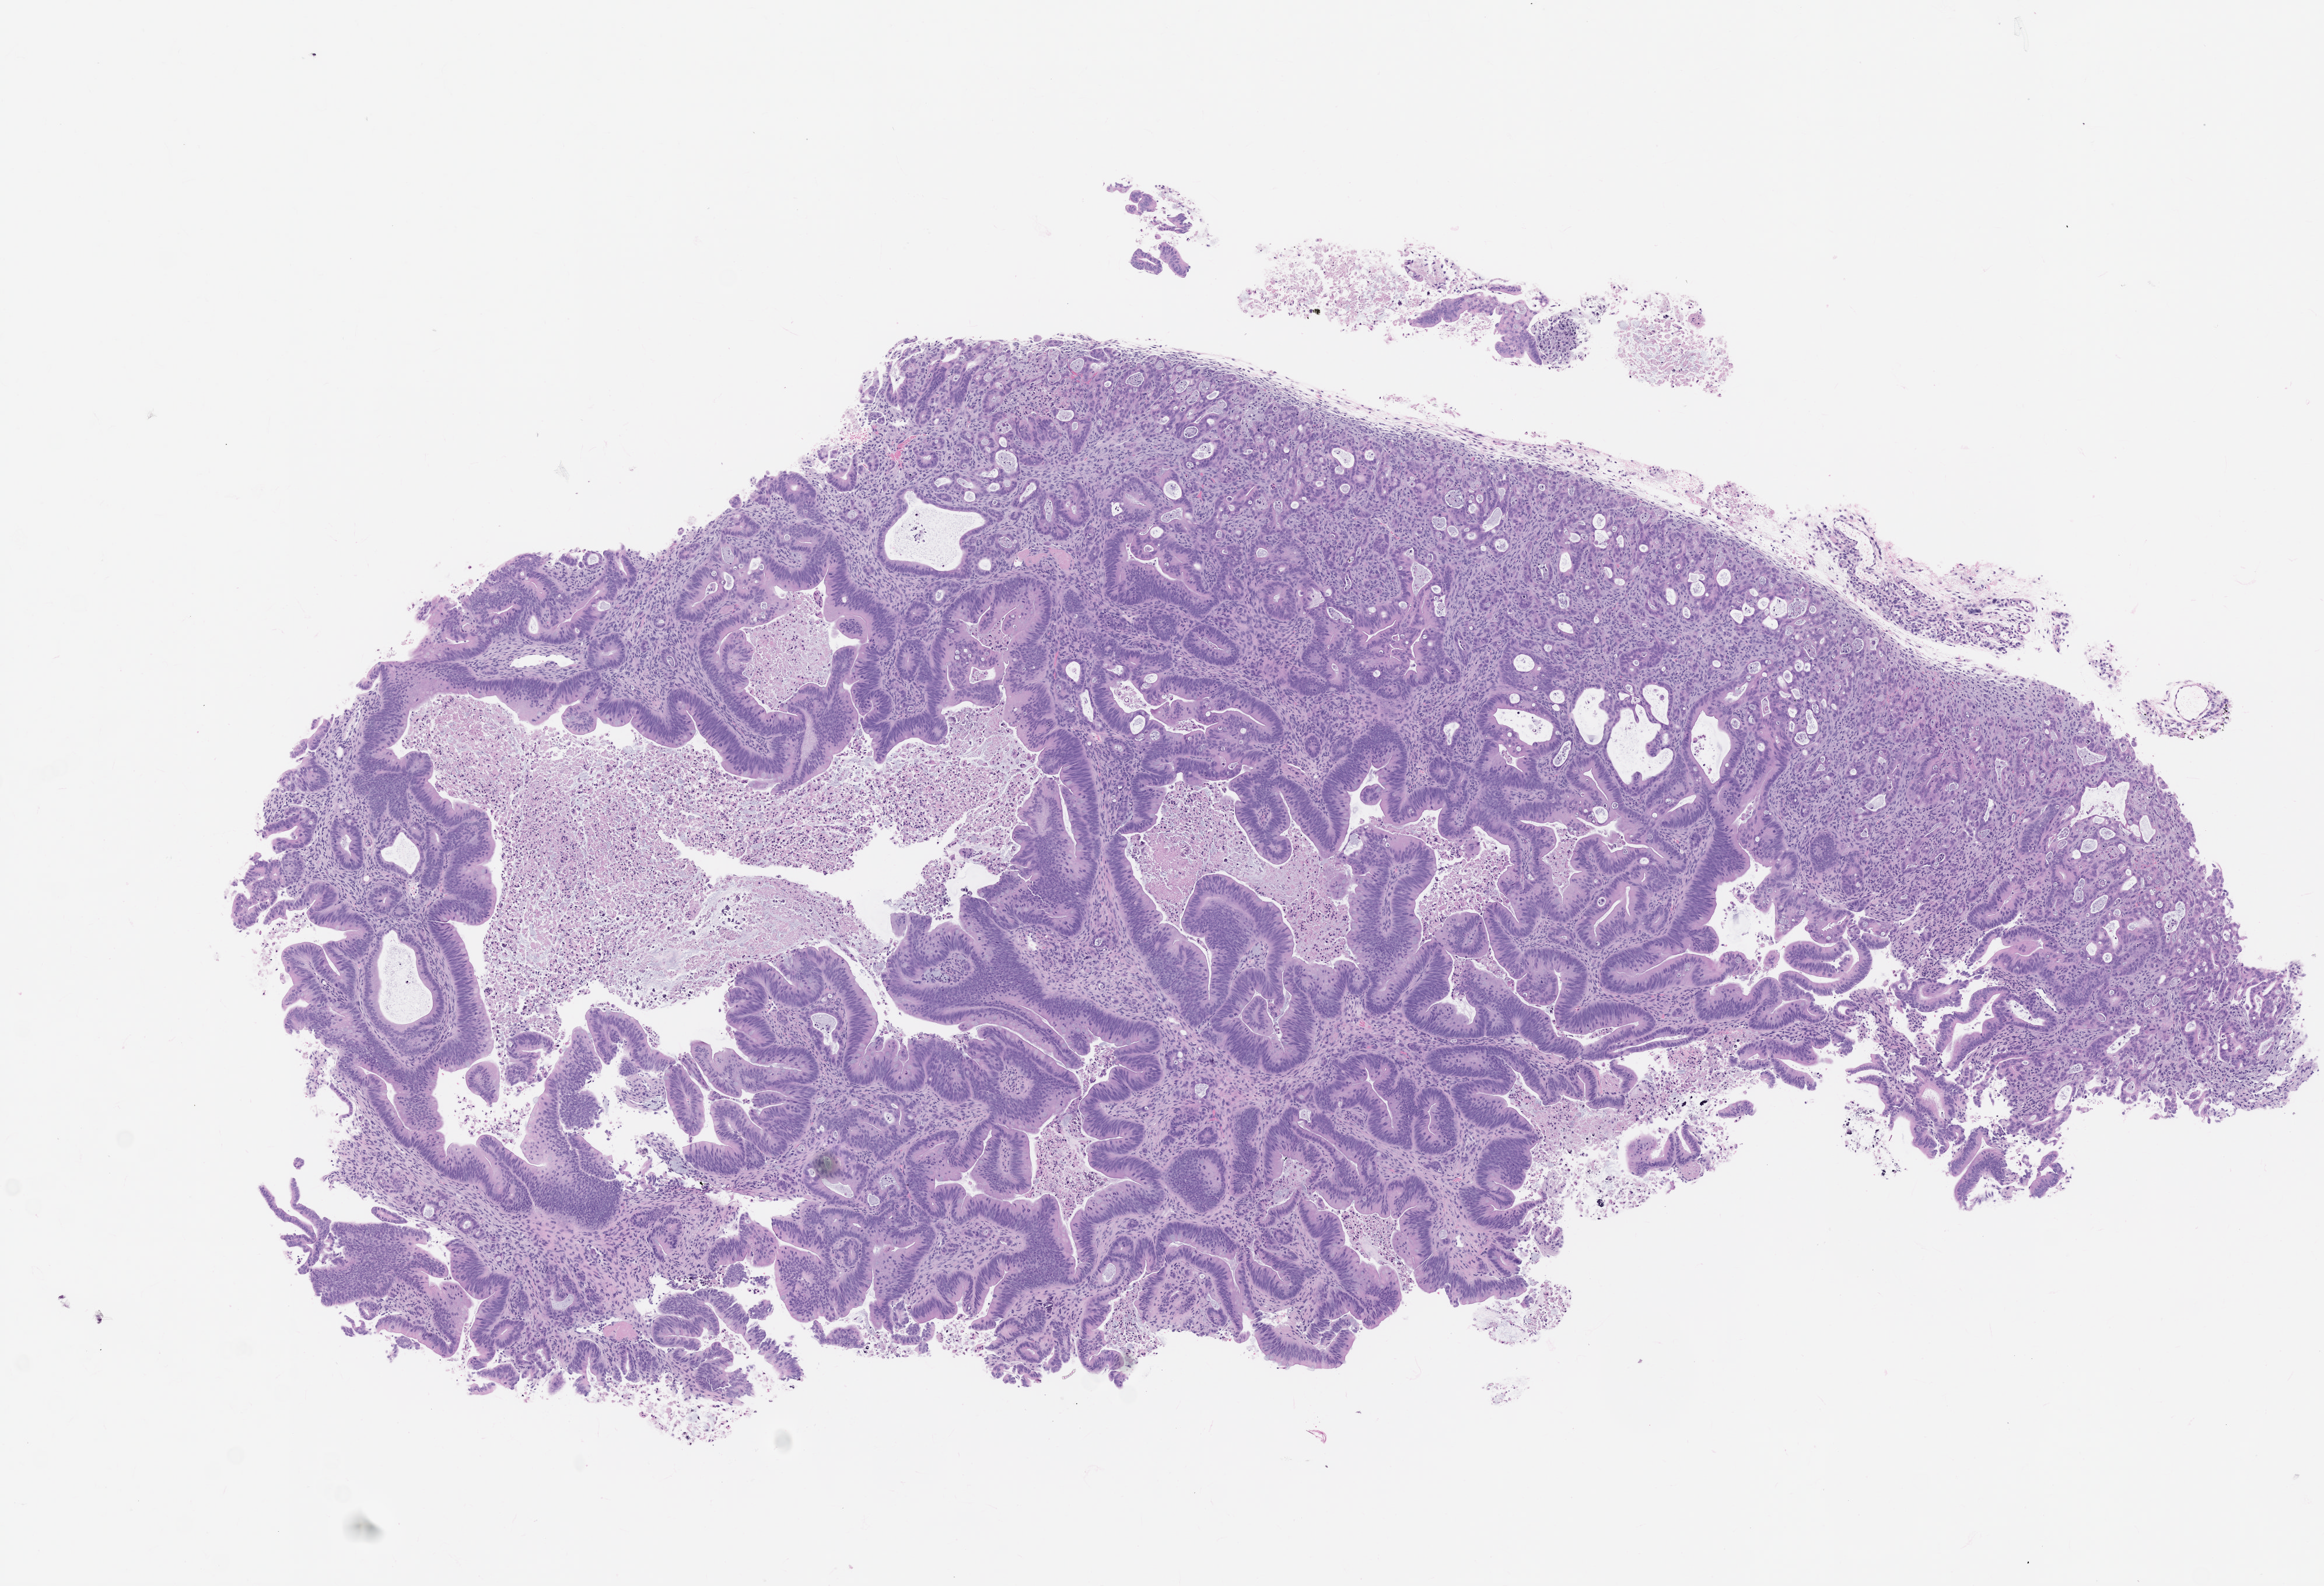
Whole-slide image, hematoxylin and eosin (H&E): patient-derived xenograft (human tumor grown in a mouse), passage 1, whole scanned area (about 8.0 x 5.5 mm) shown as a low-resolution overview. Formalin-fixed paraffin-embedded section. Originating tumor site category: colon.
Originating patient diagnosis: Colon Adenocarcinoma.